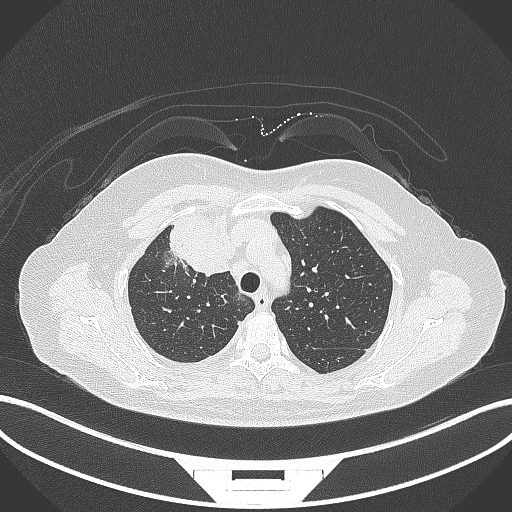
Chest CT, one axial slice; slice 232 of 305 in the series (ordered by position); reconstruction kernel B70f; 120 kVp; lung window (W 1500 / L -600 HU); 1 mm slice thickness; 512 × 512 image matrix. Female patient, age 52 years. Case-level facts recorded for this patient, not image findings: clinical TNM (as recorded): T3 N1 M1.
Structures marked on this image (rectangle marked by the reading radiologist):
- lung tumour (recorded histology: adenocarcinoma): bounding box <163,215,231,276> (left, top, right, bottom; pixels)